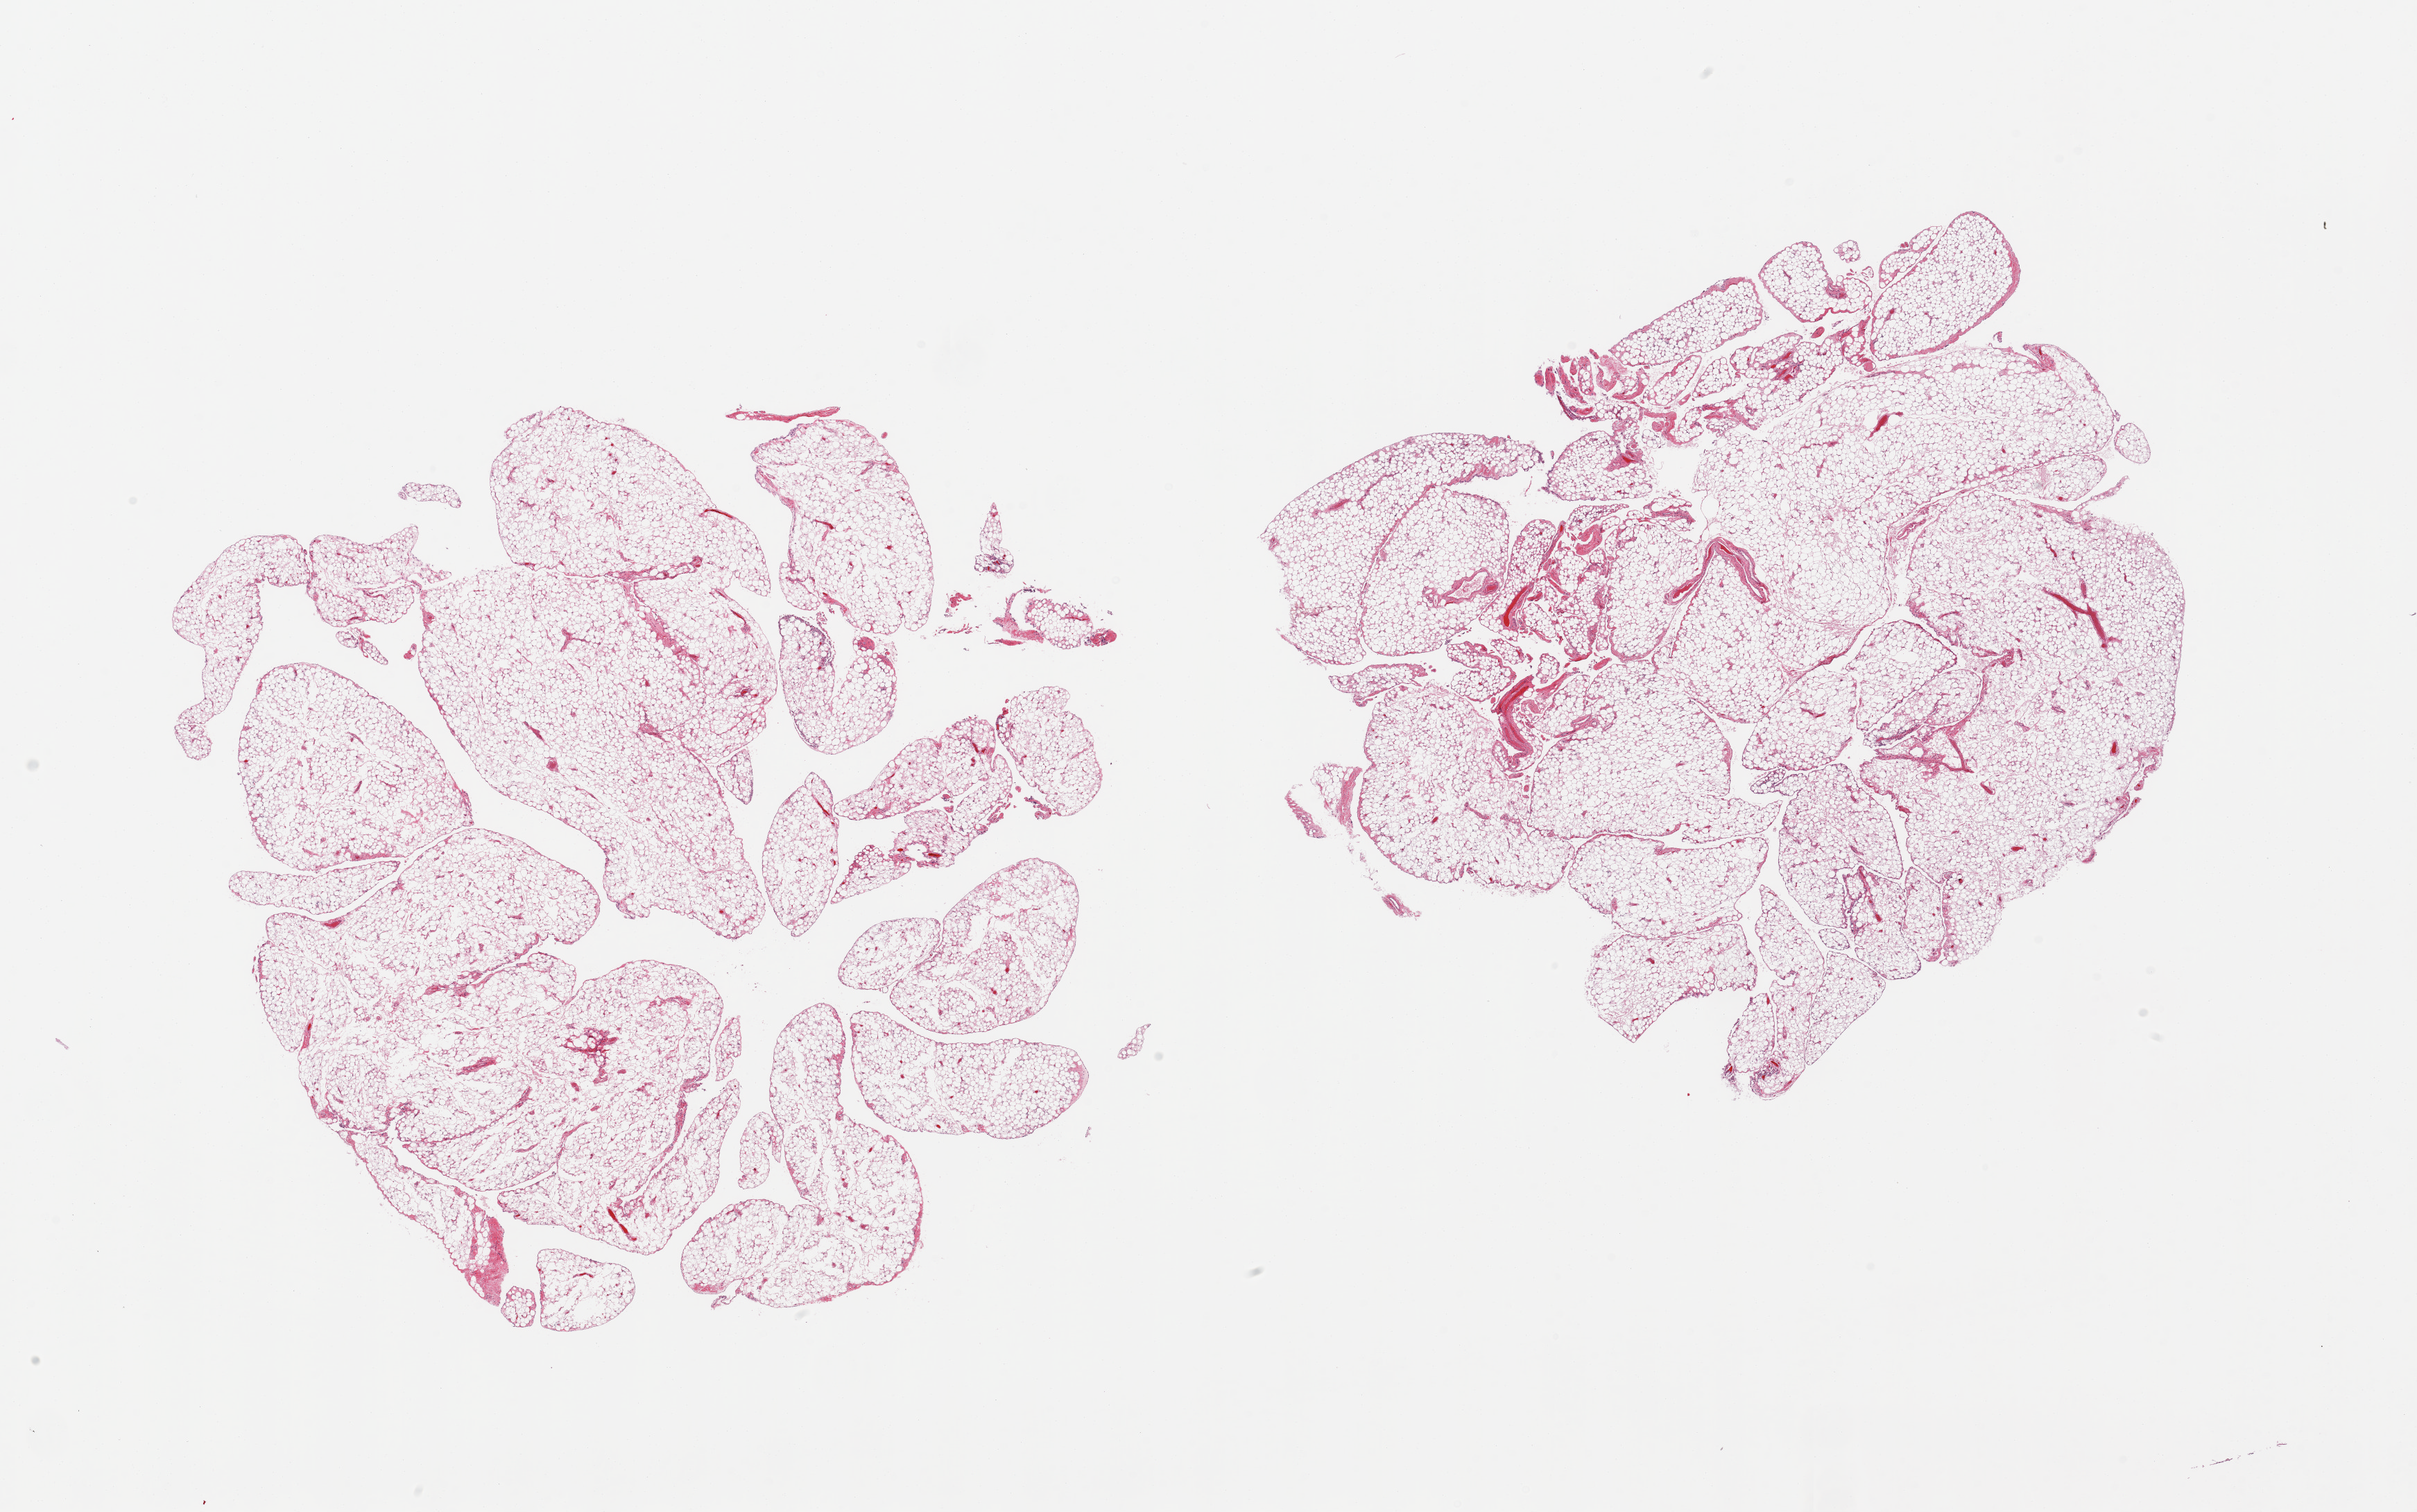
Digitized hematoxylin and eosin (H&E)-stained section, whole scanned area (about 27.6 x 17.2 mm, slide scanned at 20x) shown as a low-resolution overview. PAXgene-fixed, paraffin-embedded tissue. Sampled site (target tissue): omentum. Donor tissue sample. Male donor.
Reviewer comment on this tissue sample: 2 pieces, fascia/vascular elements are ~5-10% of tissue.